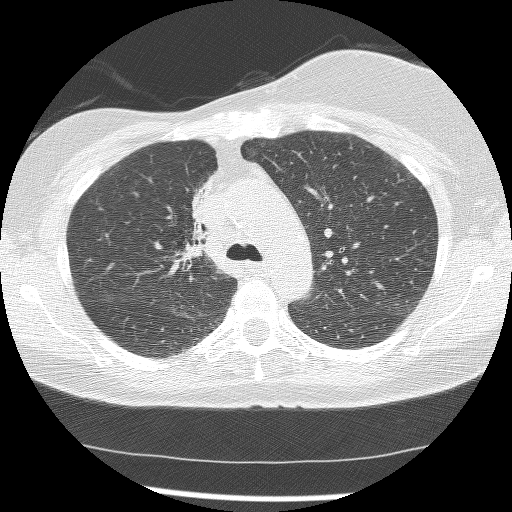
Axial slice from a low-dose chest CT screening exam. Baseline annual screen. Lung window (W 1500 / L -600 HU). 2.5 mm slice thickness. Lung (sharp) reconstruction kernel (BONE). 120 kVp. Slice 48 of 172 in the series. Female participant, aged 56 years at enrolment. Current smoker at enrolment.
• Lesion marked by an expert reader, bounding box [x1, y1, x2, y2] px = [163, 174, 220, 267].
• The screening reader recorded 2 non-calcified nodules or masses ≥4 mm on this exam; which of them this box marks is not recorded.
• Official screen result: positive, change unspecified: nodule(s) >= 4 mm or enlarging nodule(s), mass(es), or other non-specific abnormalities suspicious for lung cancer.